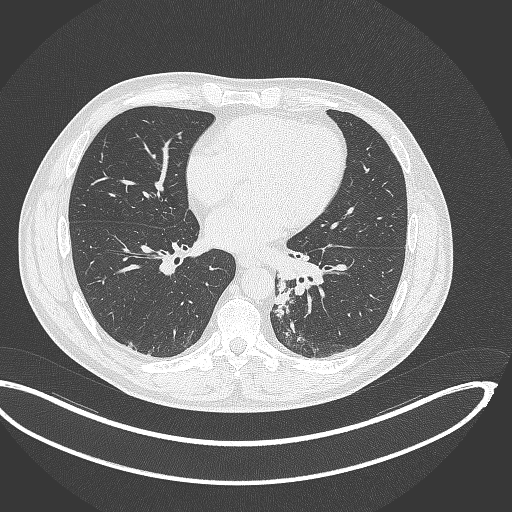
Chest CT, one axial slice; position 148 of 362 along the scan axis; reconstruction kernel B70f; 120 kVp; lung window (W 1500 / L -600 HU); 1 mm slice thickness; 512 × 512 image matrix, field of view 442 × 442 mm. Male patient, age 50 years. Case-level facts recorded for this patient, not image findings: clinical TNM (as recorded): T2a N3 M0.
Structures marked on this image (rectangle marked by the reading radiologist):
- lung tumour (recorded histology: squamous cell carcinoma): bounding box (x1, y1, x2, y2) in pixels: (272, 277, 294, 316)